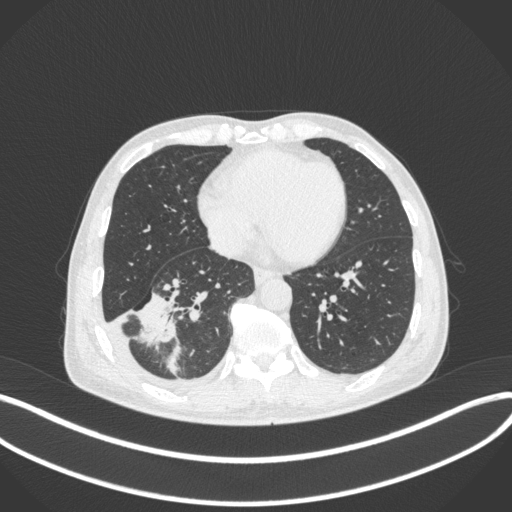
Chest CT, one axial slice. Position 135 of 385 along the scan axis. Lung window (W 1500 / L -600 HU). 1 mm slice thickness. 512 × 512 image matrix, field of view 400 × 400 mm. Patient: male, 64 years. Case-level facts recorded for this patient, not image findings: clinical TNM (as recorded): T3 N0 M0; histopathological grade: G2-3.
Structures marked on this image (rectangle marked by the reading radiologist):
- lung tumour (recorded histology: adenocarcinoma): bounding box <134,289,180,346> (left, top, right, bottom; pixels)